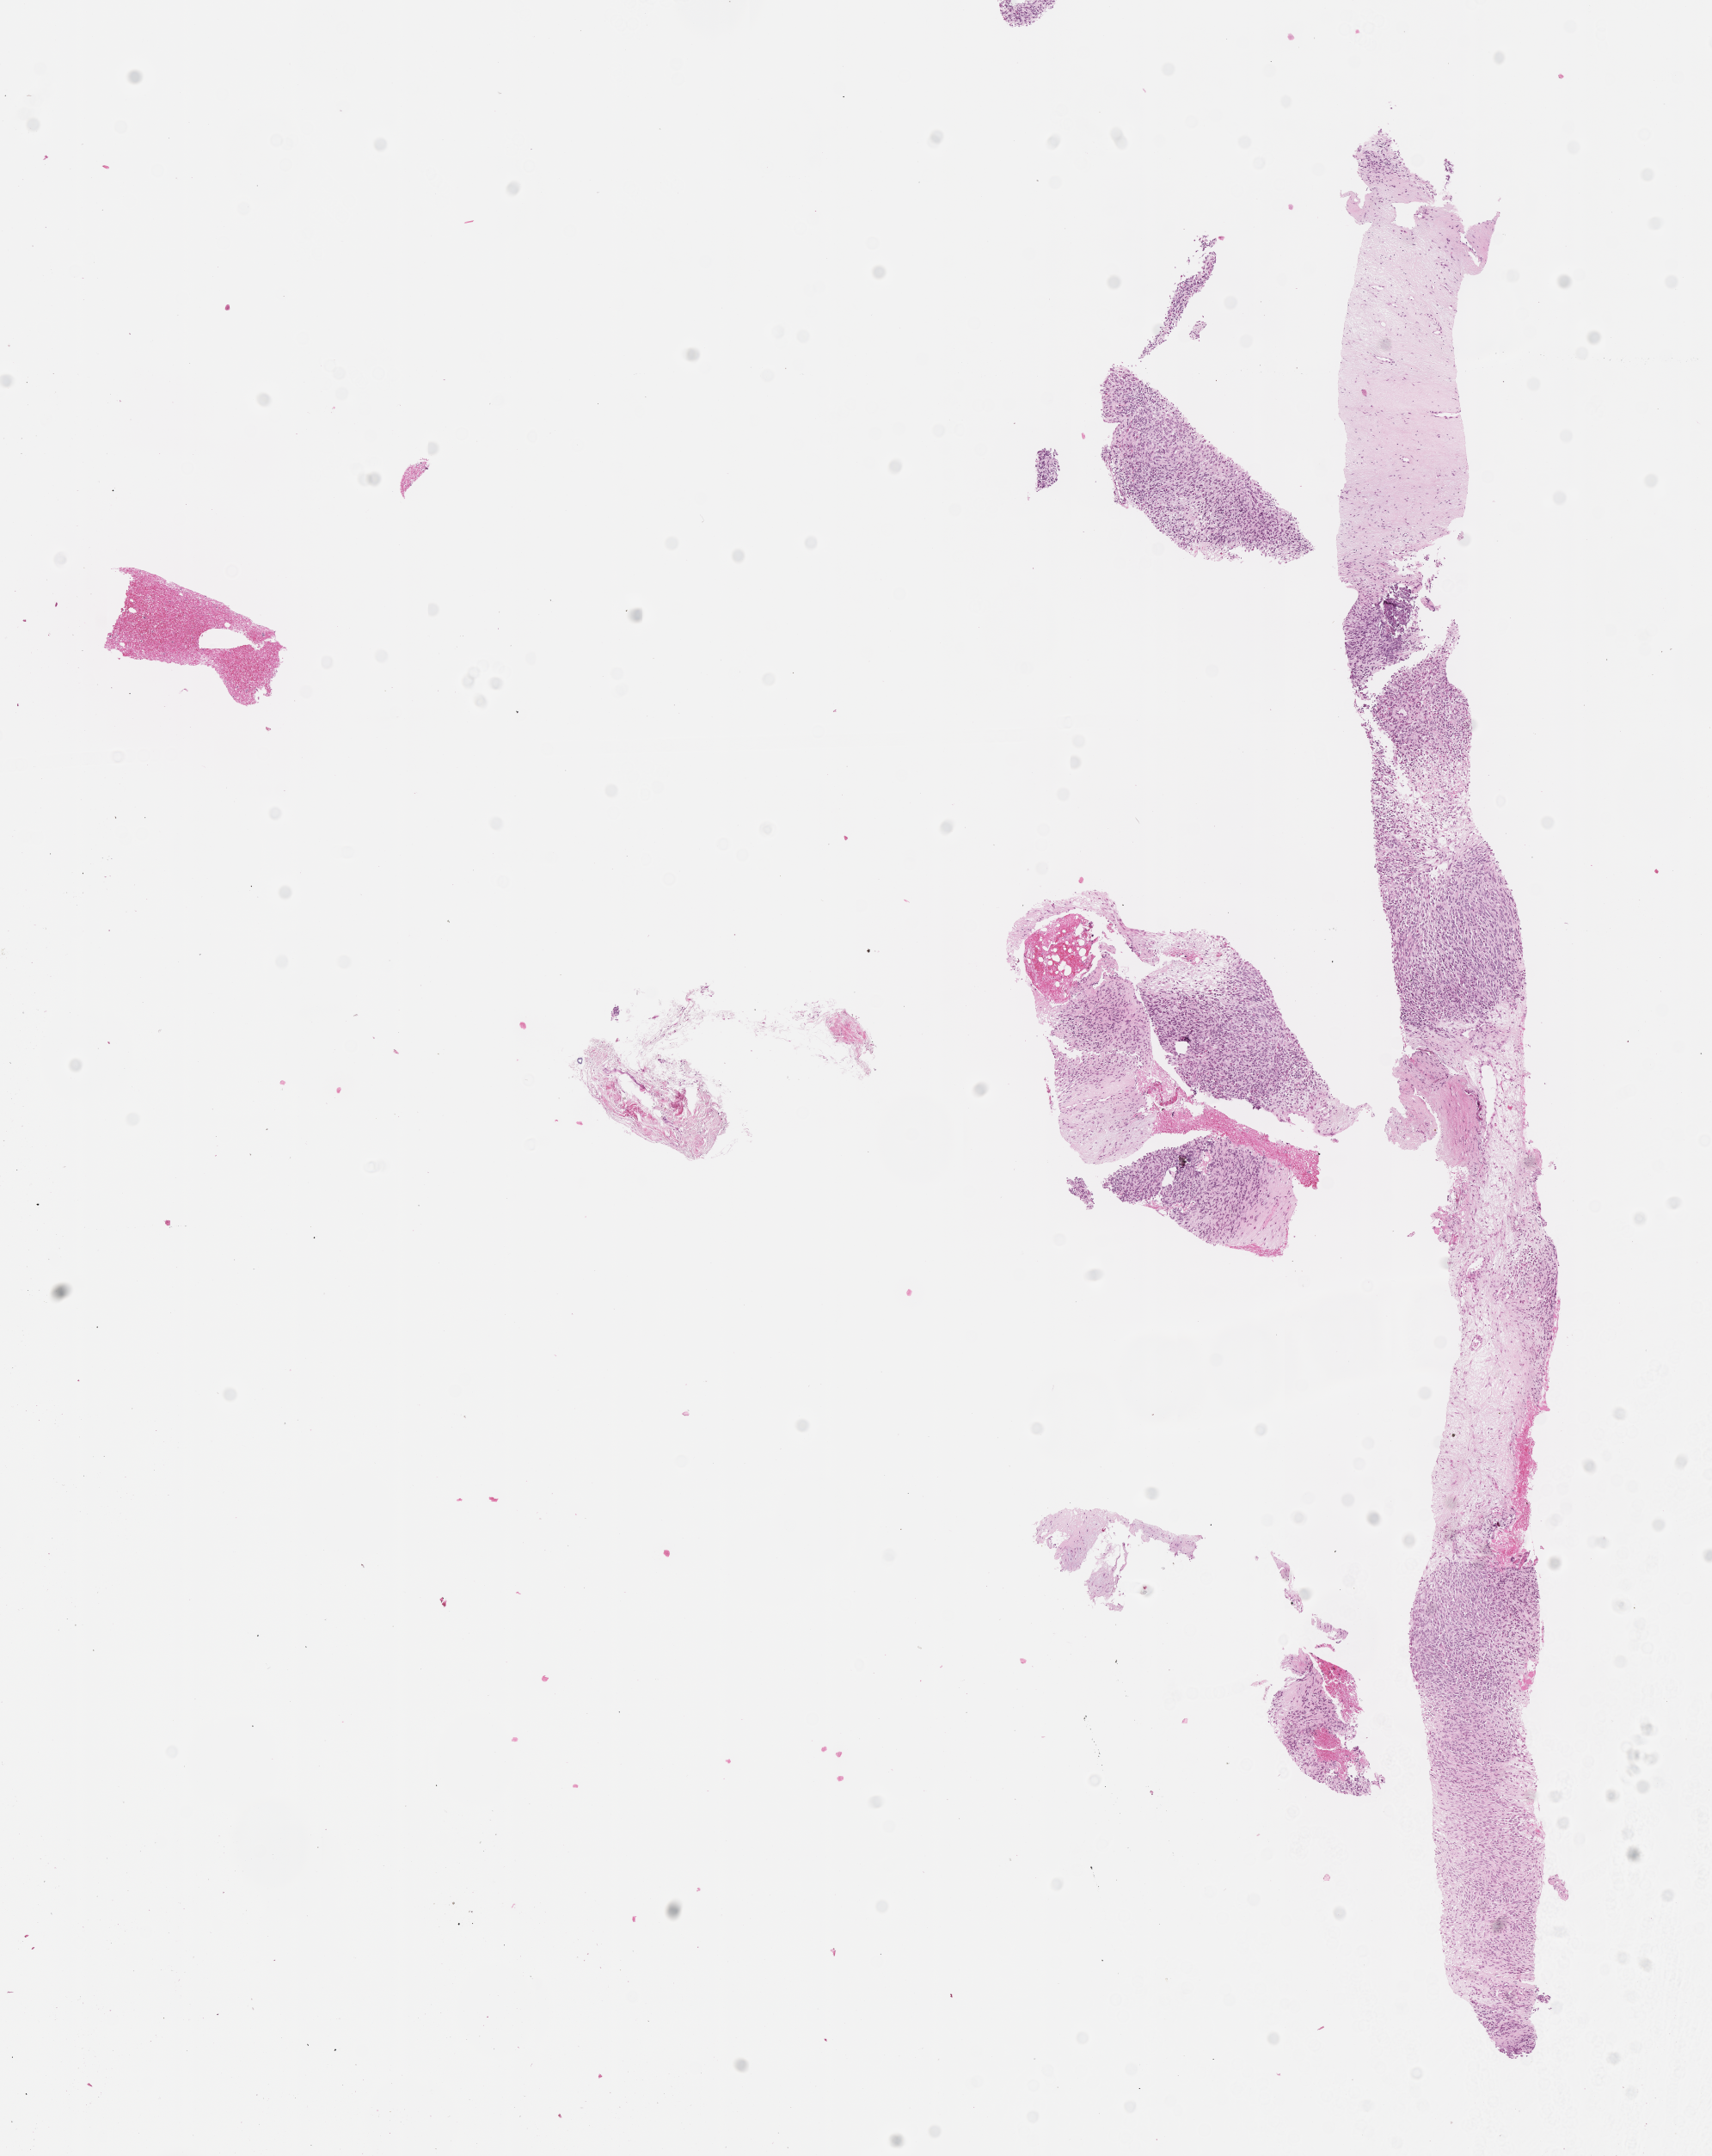
Whole-slide image, H&E stain of tumor tissue, low-resolution overview of the scanned area, about 8.1 x 10.1 mm, formalin-fixed paraffin-embedded section, site: pharynx-left (parapharyngeal). Female patient, age at diagnosis 2.2 years.
Diagnosis: rhabdomyosarcoma; histological classification: embryonal rhabdomyosarcoma.